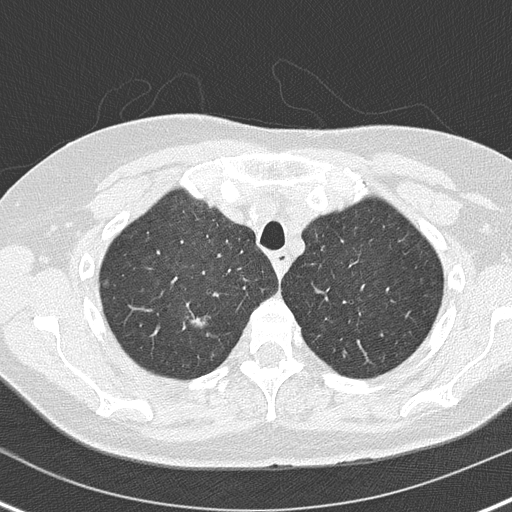
Low-dose screening chest CT, axial slice, baseline screening round, lung window (W 1500 / L -600 HU), 2 mm slice thickness. Female, age 61 years at enrolment.
Expert reader's lesion annotation, bounding box (x1, y1, x2, y2) in pixels: (183, 307, 217, 336). The exam's reader record, not a measurement of the box and not confirmed to be the same lesion: non-calcified nodule or mass ≥4 mm, right upper lobe, 8 × 5 mm, smooth margins, soft tissue attenuation. Official screen result: positive, change unspecified: nodule(s) >= 4 mm or enlarging nodule(s), mass(es), or other non-specific abnormalities suspicious for lung cancer. Later outcome: lung cancer diagnosed 438 days after this screen (after the second annual screen) — adenocarcinoma, NOS, right upper lobe, moderately differentiated (G2), stage IA (AJCC 6th edition), 20 mm at pathology.